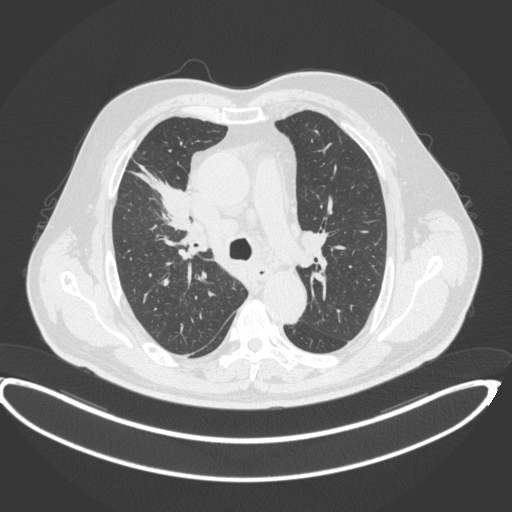
Chest CT, one axial slice. Slice 275 of 395 in the series (ordered by position). 120 kVp. Lung window (W 1500 / L -600 HU). 1 mm slice thickness. 512 × 512 image matrix, field of view 448 × 448 mm. Patient: male, 62 years. Case-level facts recorded for this patient, not image findings: clinical TNM (as recorded): T1c N3 M1c.
Outlined on this slice (bounding box drawn by a radiologist):
- lung tumour (recorded histology: adenocarcinoma): box from (x=129, y=159) to (x=194, y=229) px